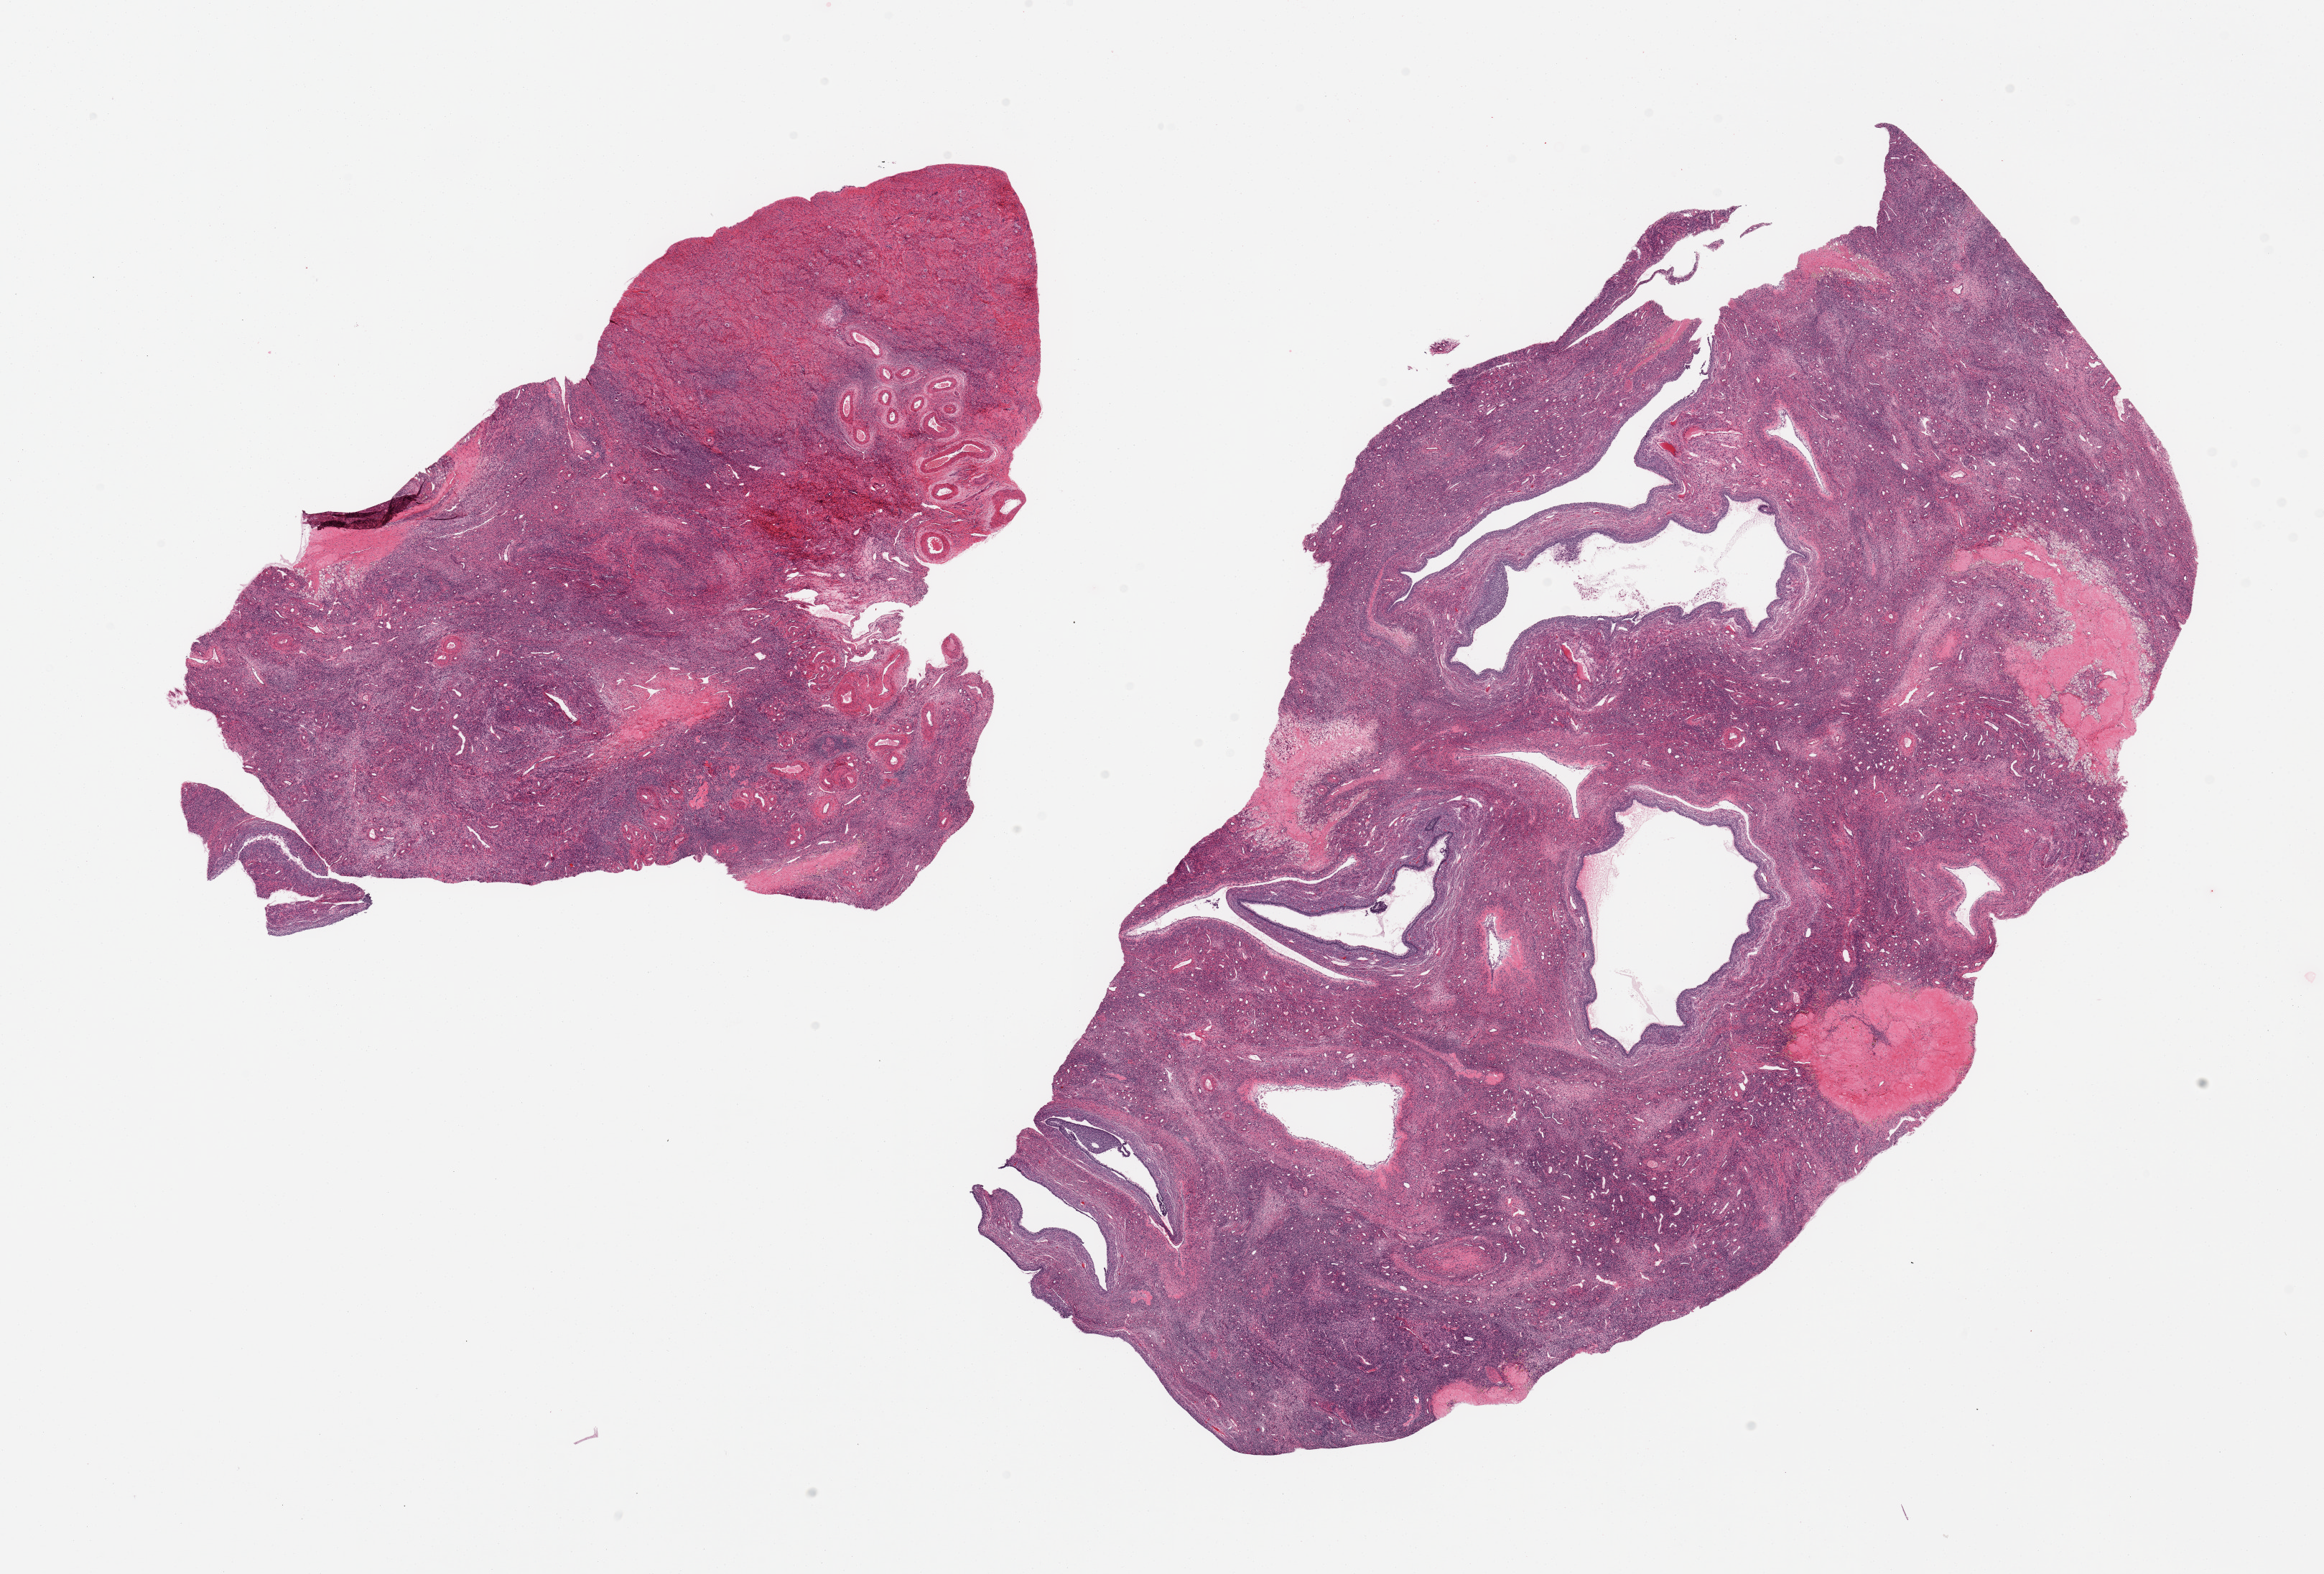
Whole-slide image, haematoxylin and eosin stain, a low-resolution overview of the entire scanned area, about 25.6 x 17.3 mm; PAXgene-fixed paraffin-embedded (PFPE) section; section of ovary (target tissue); tissue donor sample. Donor: female.
• pathologist's review note for this sample: 2 pieces, incidental follicular cysts viable eggs still visible